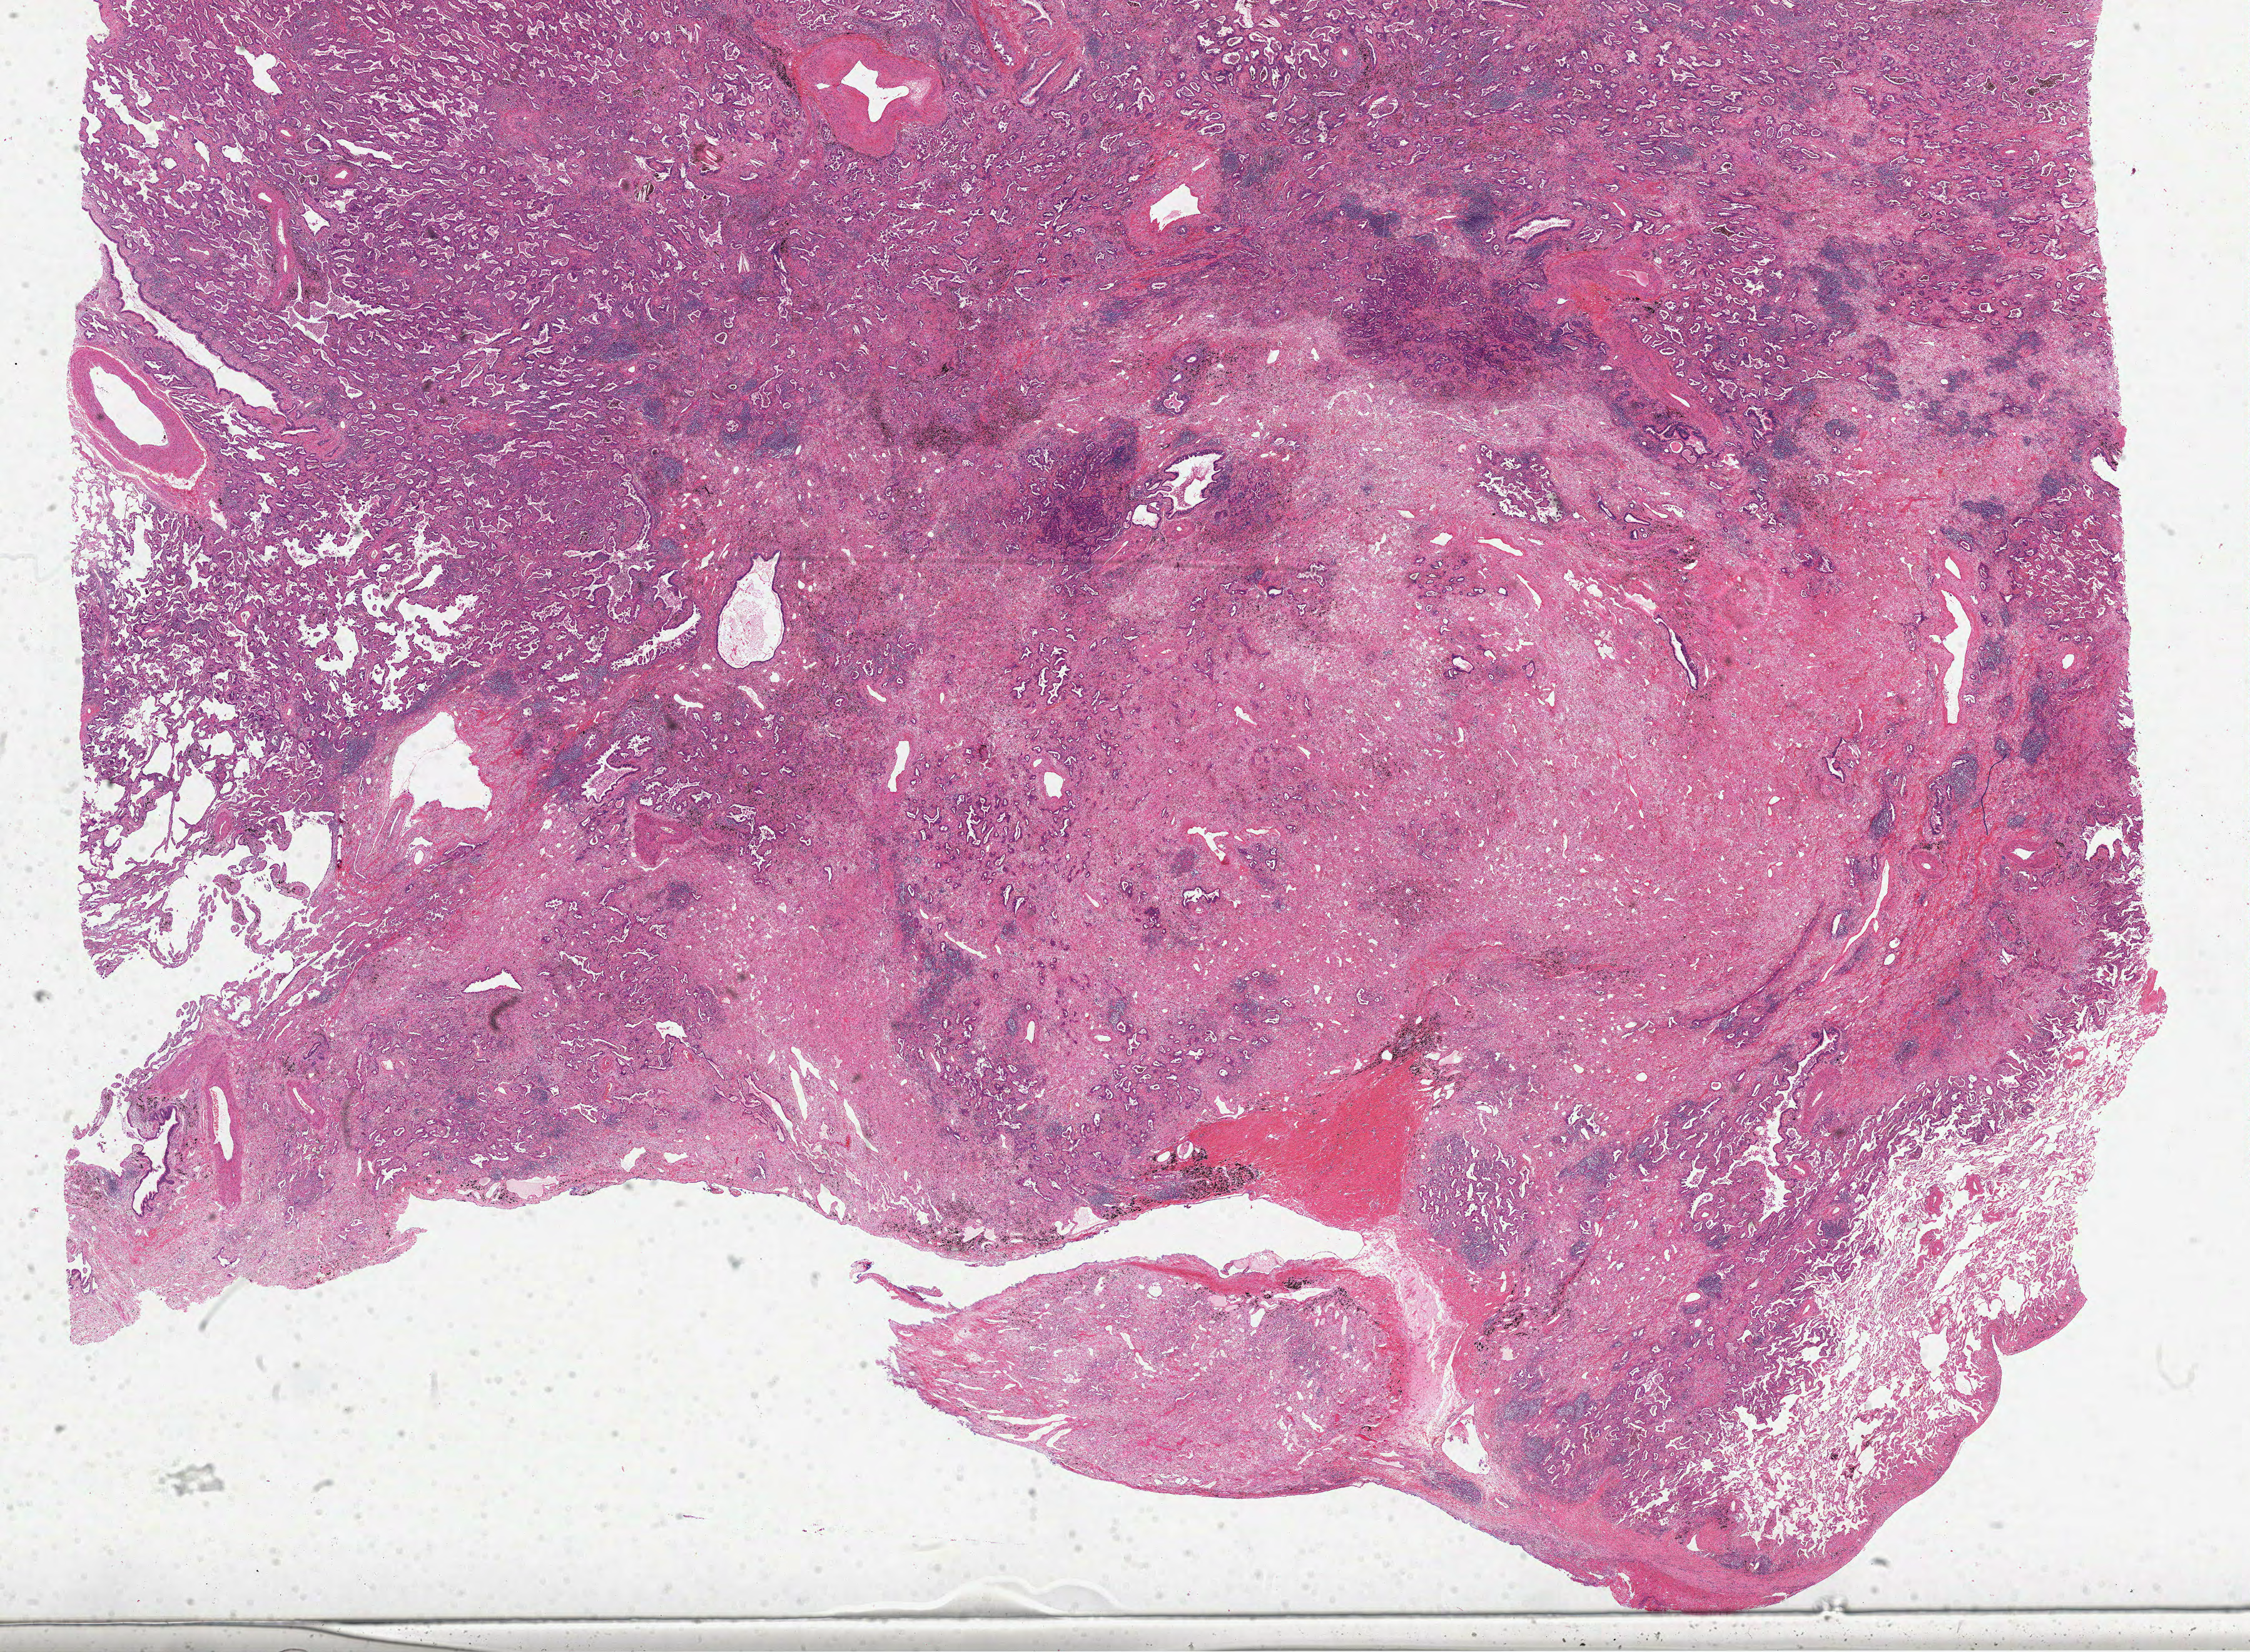
H&E-stained whole-slide image, a low-resolution overview of the entire scanned area, about 29.0 x 21.3 mm; formalin-fixed paraffin-embedded (FFPE) diagnostic section; sample: primary tumour, lung. Female, age 67 years at initial diagnosis.
Laterality: right. TNM: T2 N1 M0. AJCC pathologic stage: IIB (6th edition). Histologic diagnosis: Adenocarcinoma, NOS (upper lobe, lung).